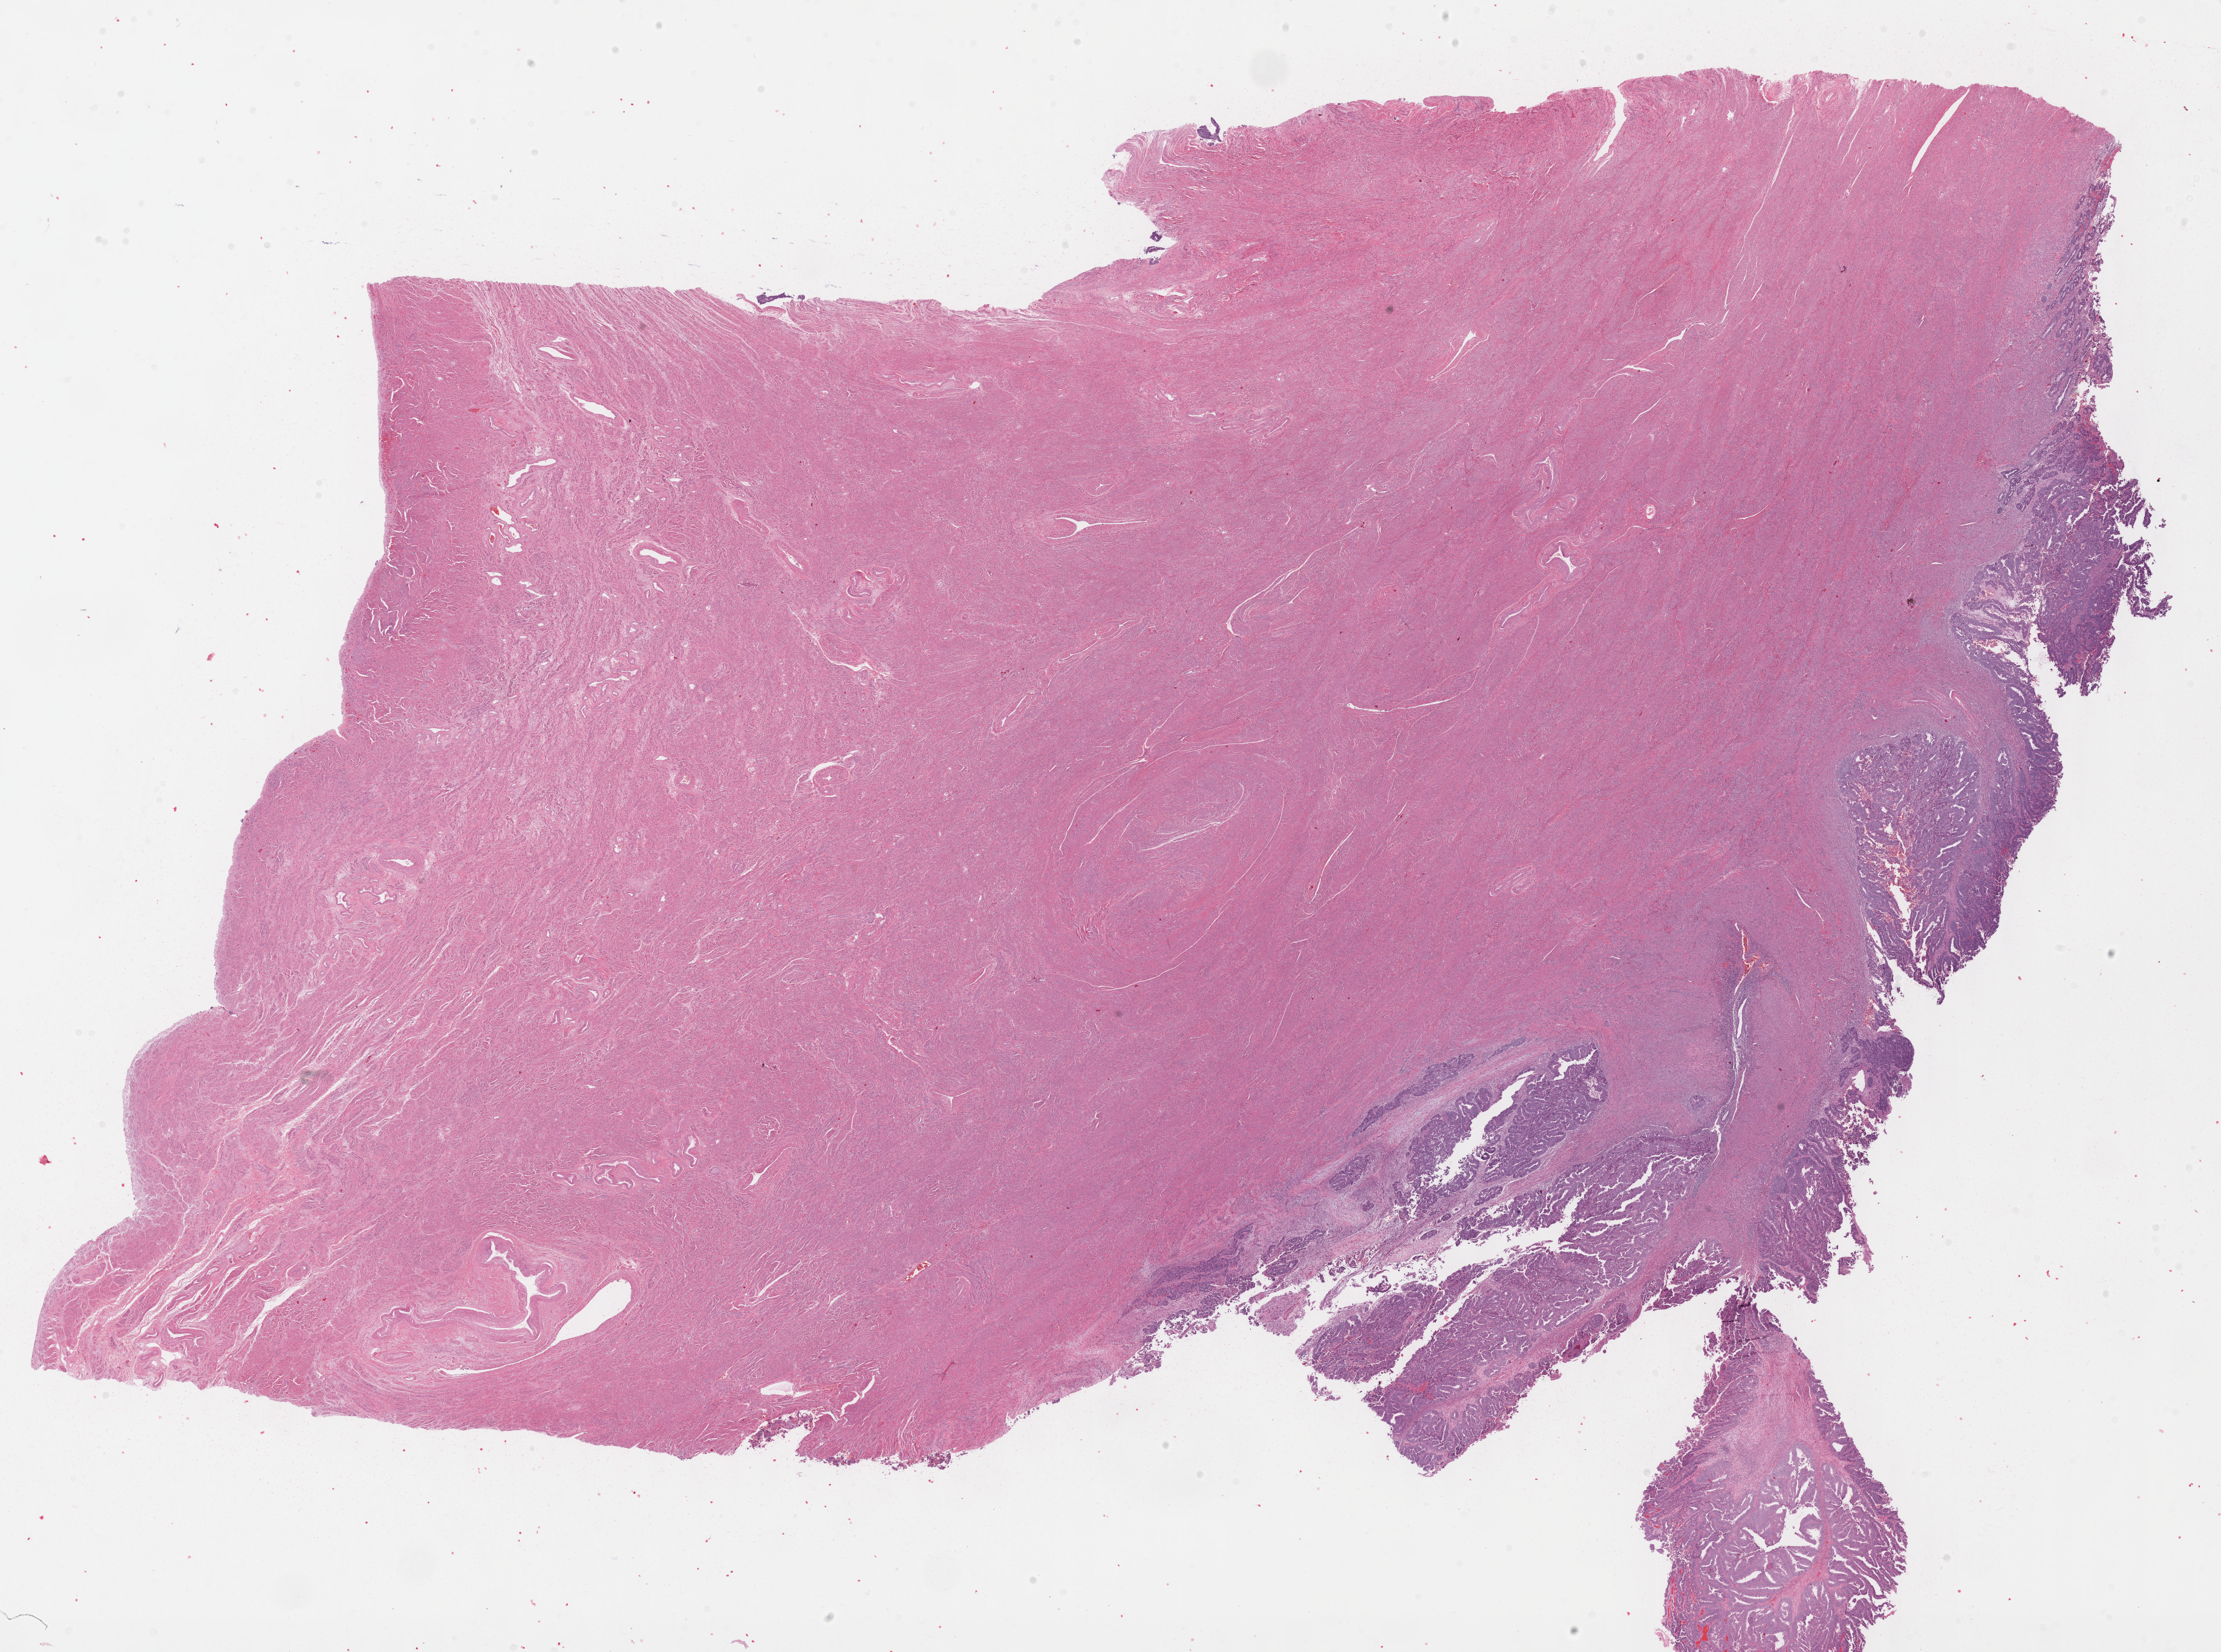
Digitized Hematoxylin and eosin (H&E) stained tissue section (whole slide) — shown as a low-resolution overview of the whole scanned area (about 29.7 x 22.1 mm, acquisition: 40x scan), formalin-fixed paraffin-embedded (FFPE) diagnostic section, primary tumour sample from the uterus. Female patient; age at initial diagnosis 69 years. Histologic grade: G2 (moderately differentiated).
• FIGO stage: IA
• diagnosis: Endometrioid adenocarcinoma, NOS (endometrium)